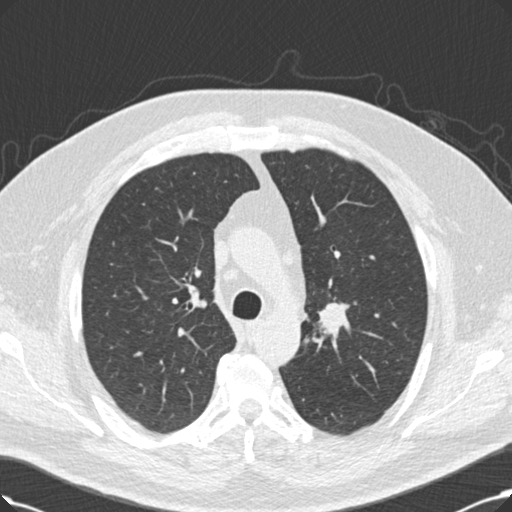
Low-dose screening chest CT, one axial slice. Position 157 of 214 along the scan axis. Reconstruction kernel B30f. Lung window (W 1500 / L -600 HU). 2 mm slice thickness. 512 × 512 image matrix.
Annotated regions visible in this slice (outlined manually by an expert reader):
- lesion 1 (tumor): box from (x=319, y=303) to (x=348, y=334) px